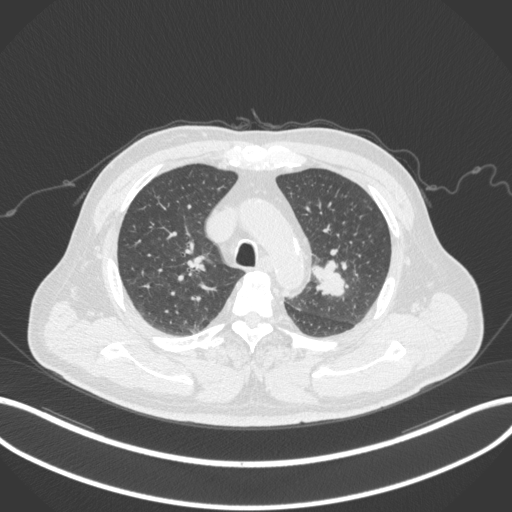
Chest CT, one axial slice; slice 224 of 286 in the series (ordered by position); reconstruction kernel B31f; lung window (W 1500 / L -600 HU); 1 mm slice thickness; 512 × 512 image matrix. Male patient, age 67 years. Case-level facts recorded for this patient, not image findings: clinical TNM (as recorded): T2a N1 M0; histopathological grade: G3.
Structures marked on this image (bounding box drawn by a radiologist):
- lung tumour (recorded histology: adenocarcinoma): box from (x=312, y=260) to (x=347, y=298) px